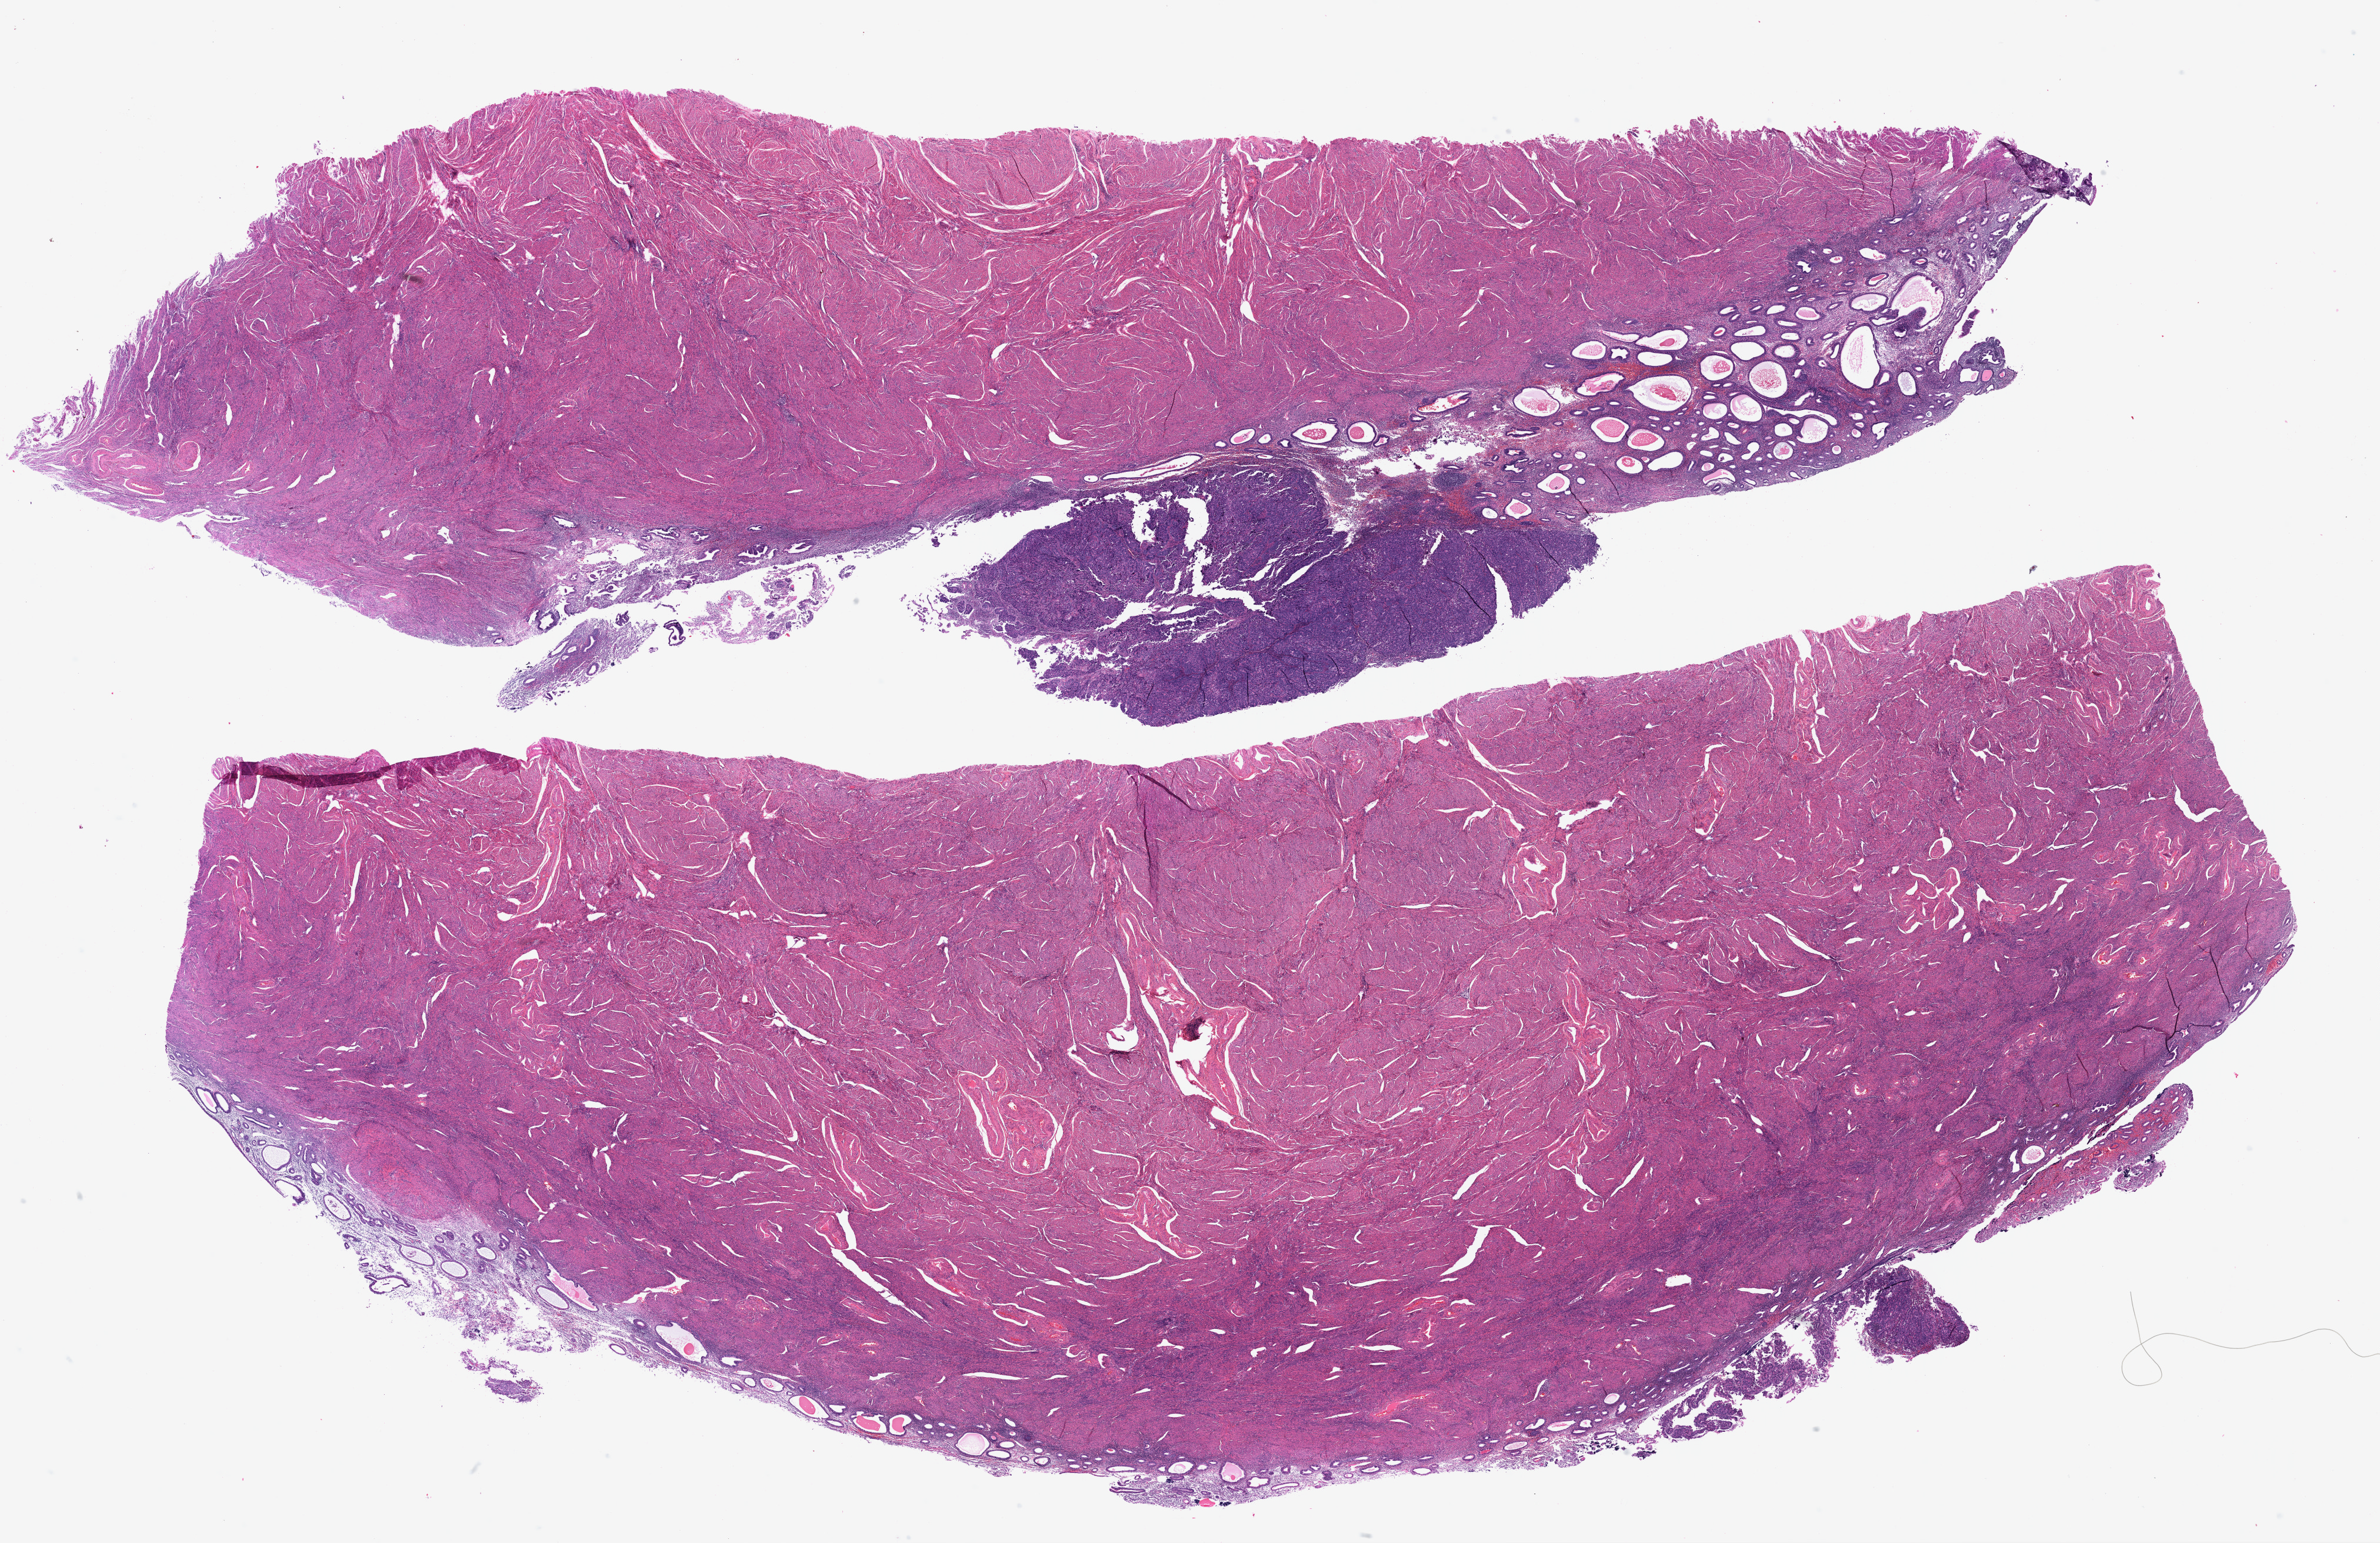
Whole-slide histology image, H&E-stained, whole scanned area (about 31.8 x 20.6 mm, acquisition: 40x scan) shown as a low-resolution overview. Formalin-fixed paraffin-embedded (FFPE) diagnostic section. Uterus, primary tumour sample. Patient: female, age at initial diagnosis 53 years. Histologic grade: G3 (poorly differentiated).
FIGO stage: II. Pathologic diagnosis: Endometrioid adenocarcinoma, NOS (endometrium).